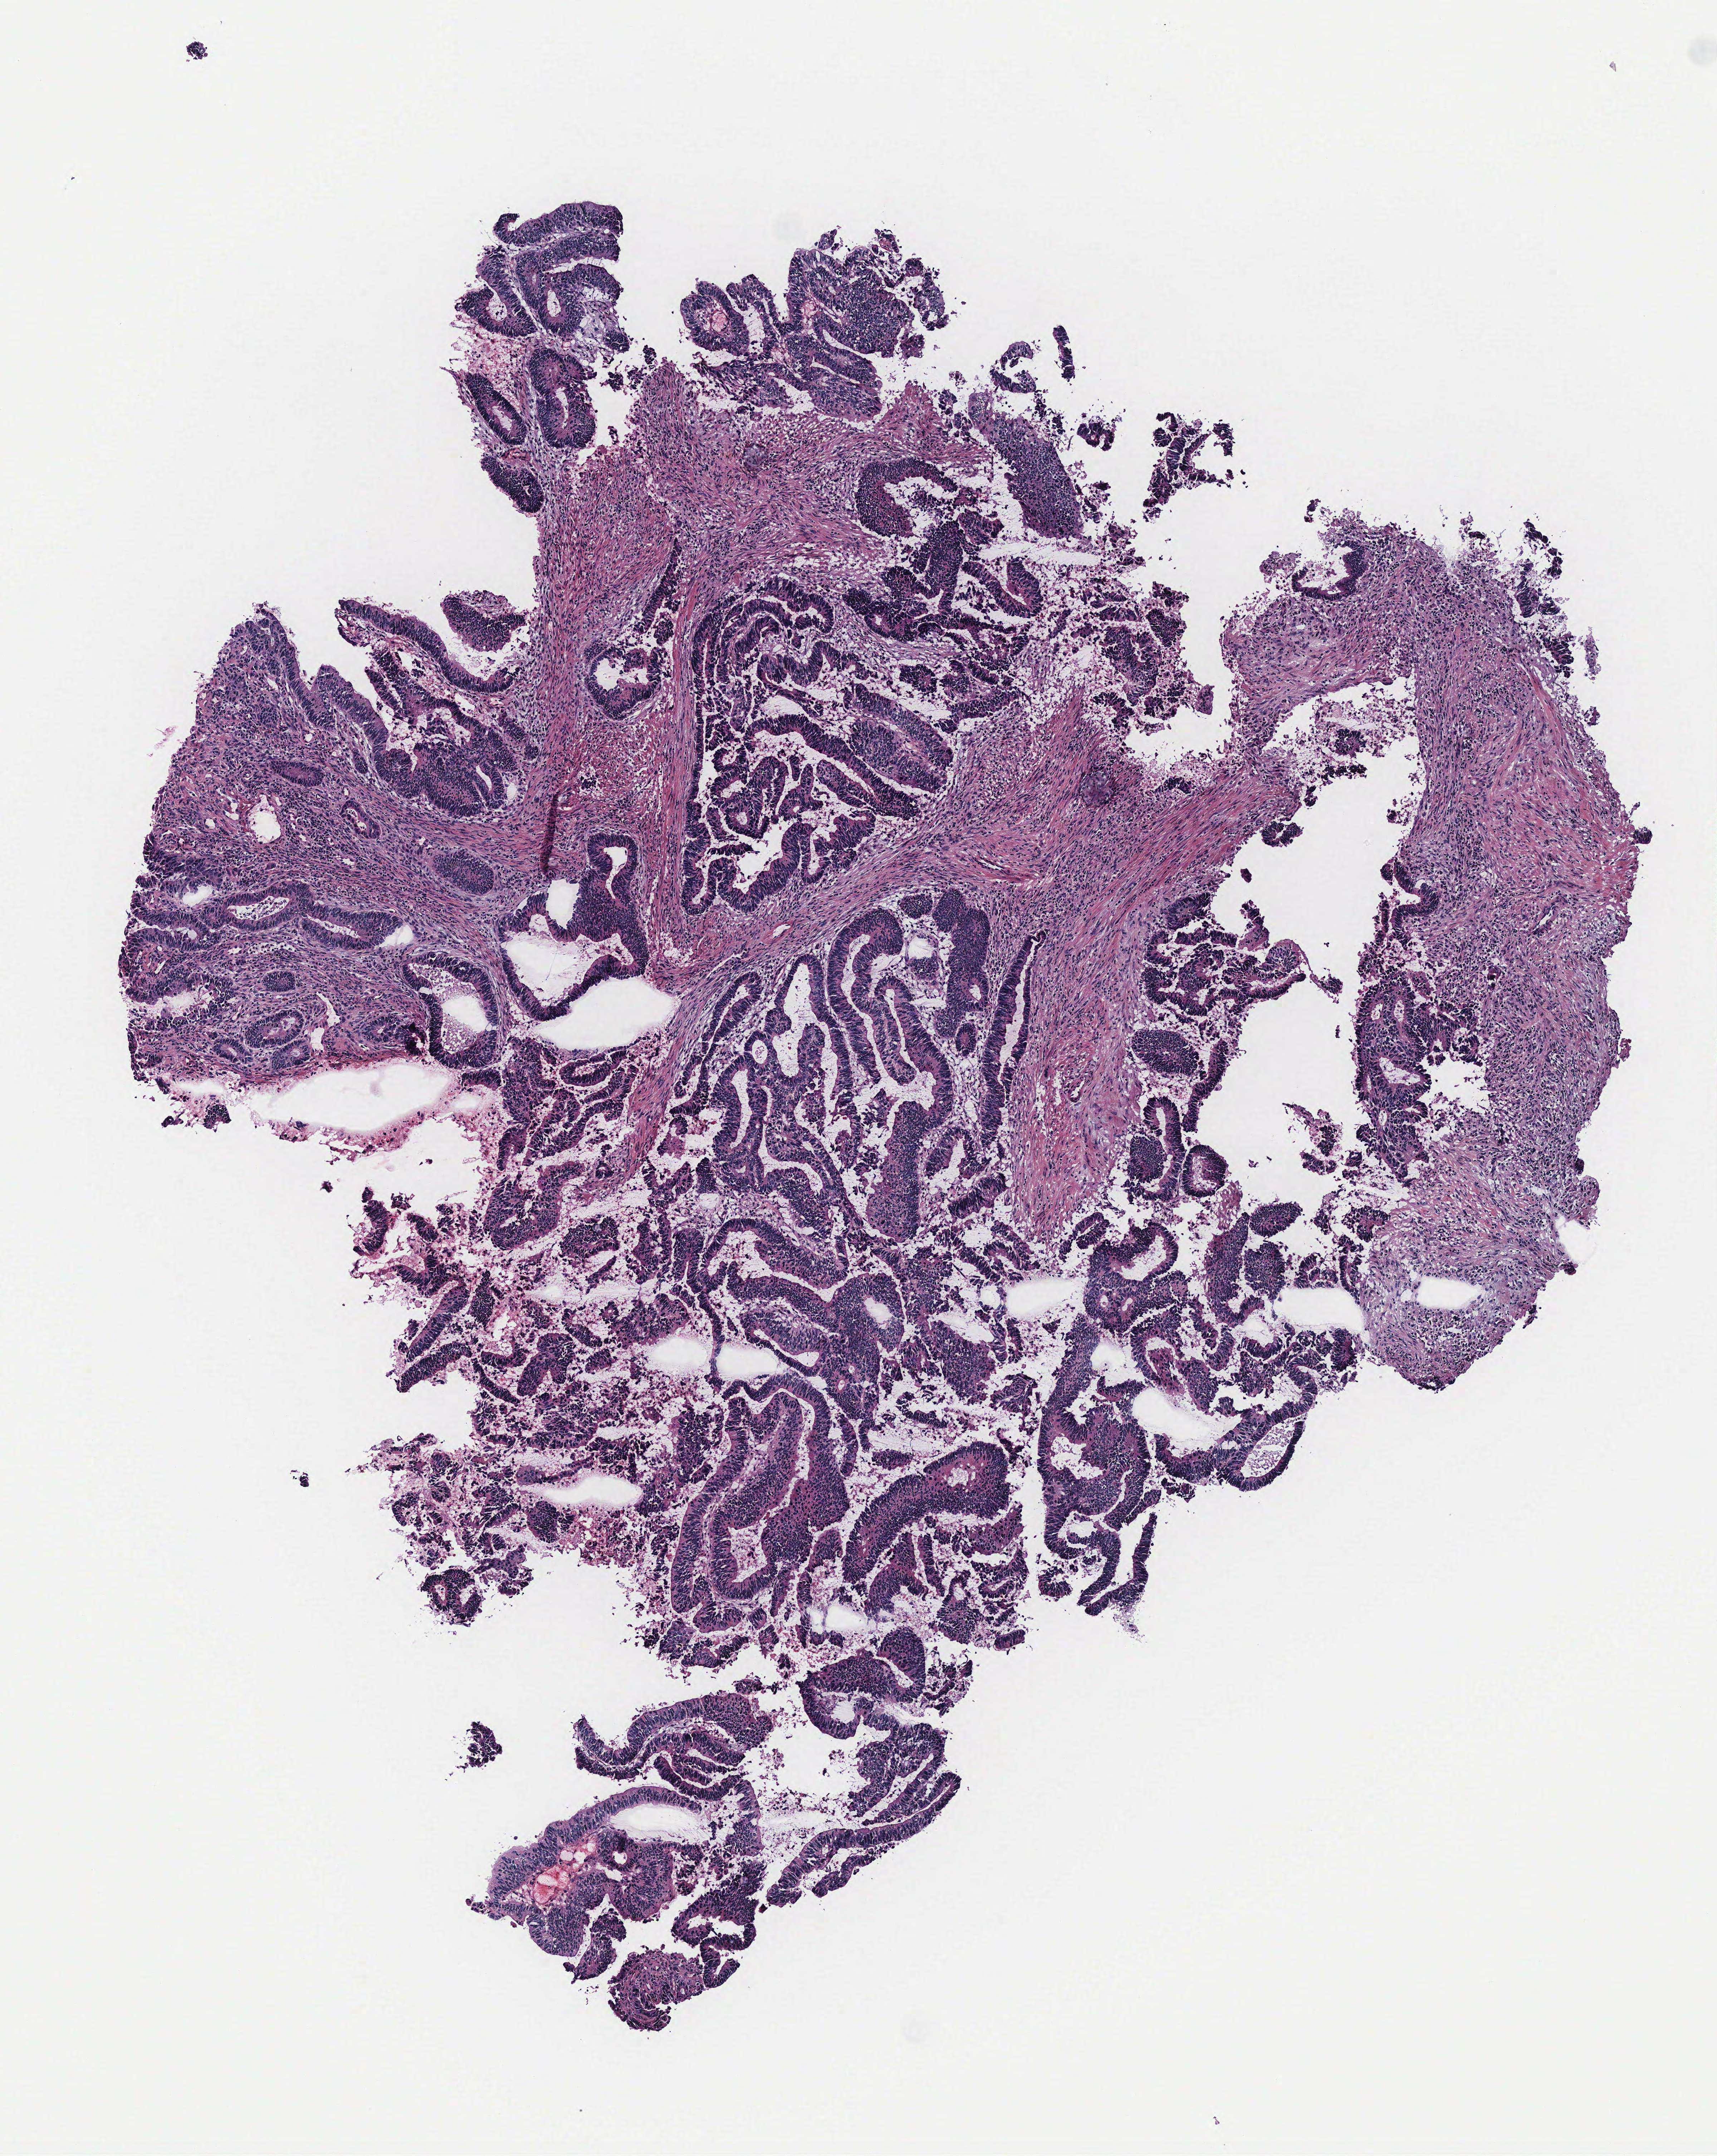
Digitized Hematoxylin and eosin (H&E) stained tissue section (whole slide) — a low-resolution overview of the entire scanned area, about 4.8 x 6.0 mm (slide scanned at 40x), colon, tissue type not recorded.
Patient diagnosis (cohort enrolment): colon cancer (colon).